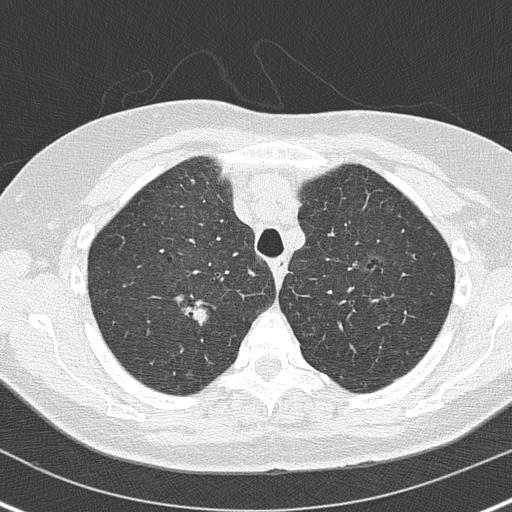
Low-dose screening chest CT, axial slice; baseline screening round; lung window (W 1500 / L -600 HU); 120 kVp; slice 38 of 162 in the series. Female participant, aged 61 years at enrolment.
• Lesion marked by an expert reader, bounding box (x1, y1, x2, y2) in pixels: (179, 292, 220, 329).
• The exam's reader record, not a measurement of the box and not confirmed to be the same lesion: non-calcified nodule or mass ≥4 mm, right upper lobe, 8 × 5 mm, smooth margins, soft tissue attenuation.
• Participant outcome: lung cancer diagnosed 438 days after this screen (after the second annual screen) — adenocarcinoma, NOS, right upper lobe, moderately differentiated (G2), stage IA (AJCC 6th edition), 20 mm at pathology.